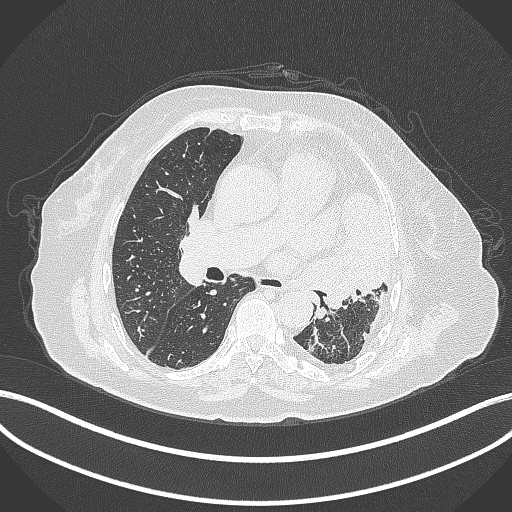
Chest CT, one axial slice. Position 201 of 399 along the scan axis. Reconstruction kernel B70f. 120 kVp. Lung window (W 1500 / L -600 HU). 1 mm slice thickness. 512 × 512 image matrix, field of view 400 × 400 mm. Patient: female, 75 years. From the clinical record (not read from this slice): clinical TNM (as recorded): T3 N3 M1.
Annotated regions visible in this slice (bounding box drawn by a radiologist):
- lung tumour (recorded histology: adenocarcinoma): box from (x=294, y=193) to (x=403, y=311) px